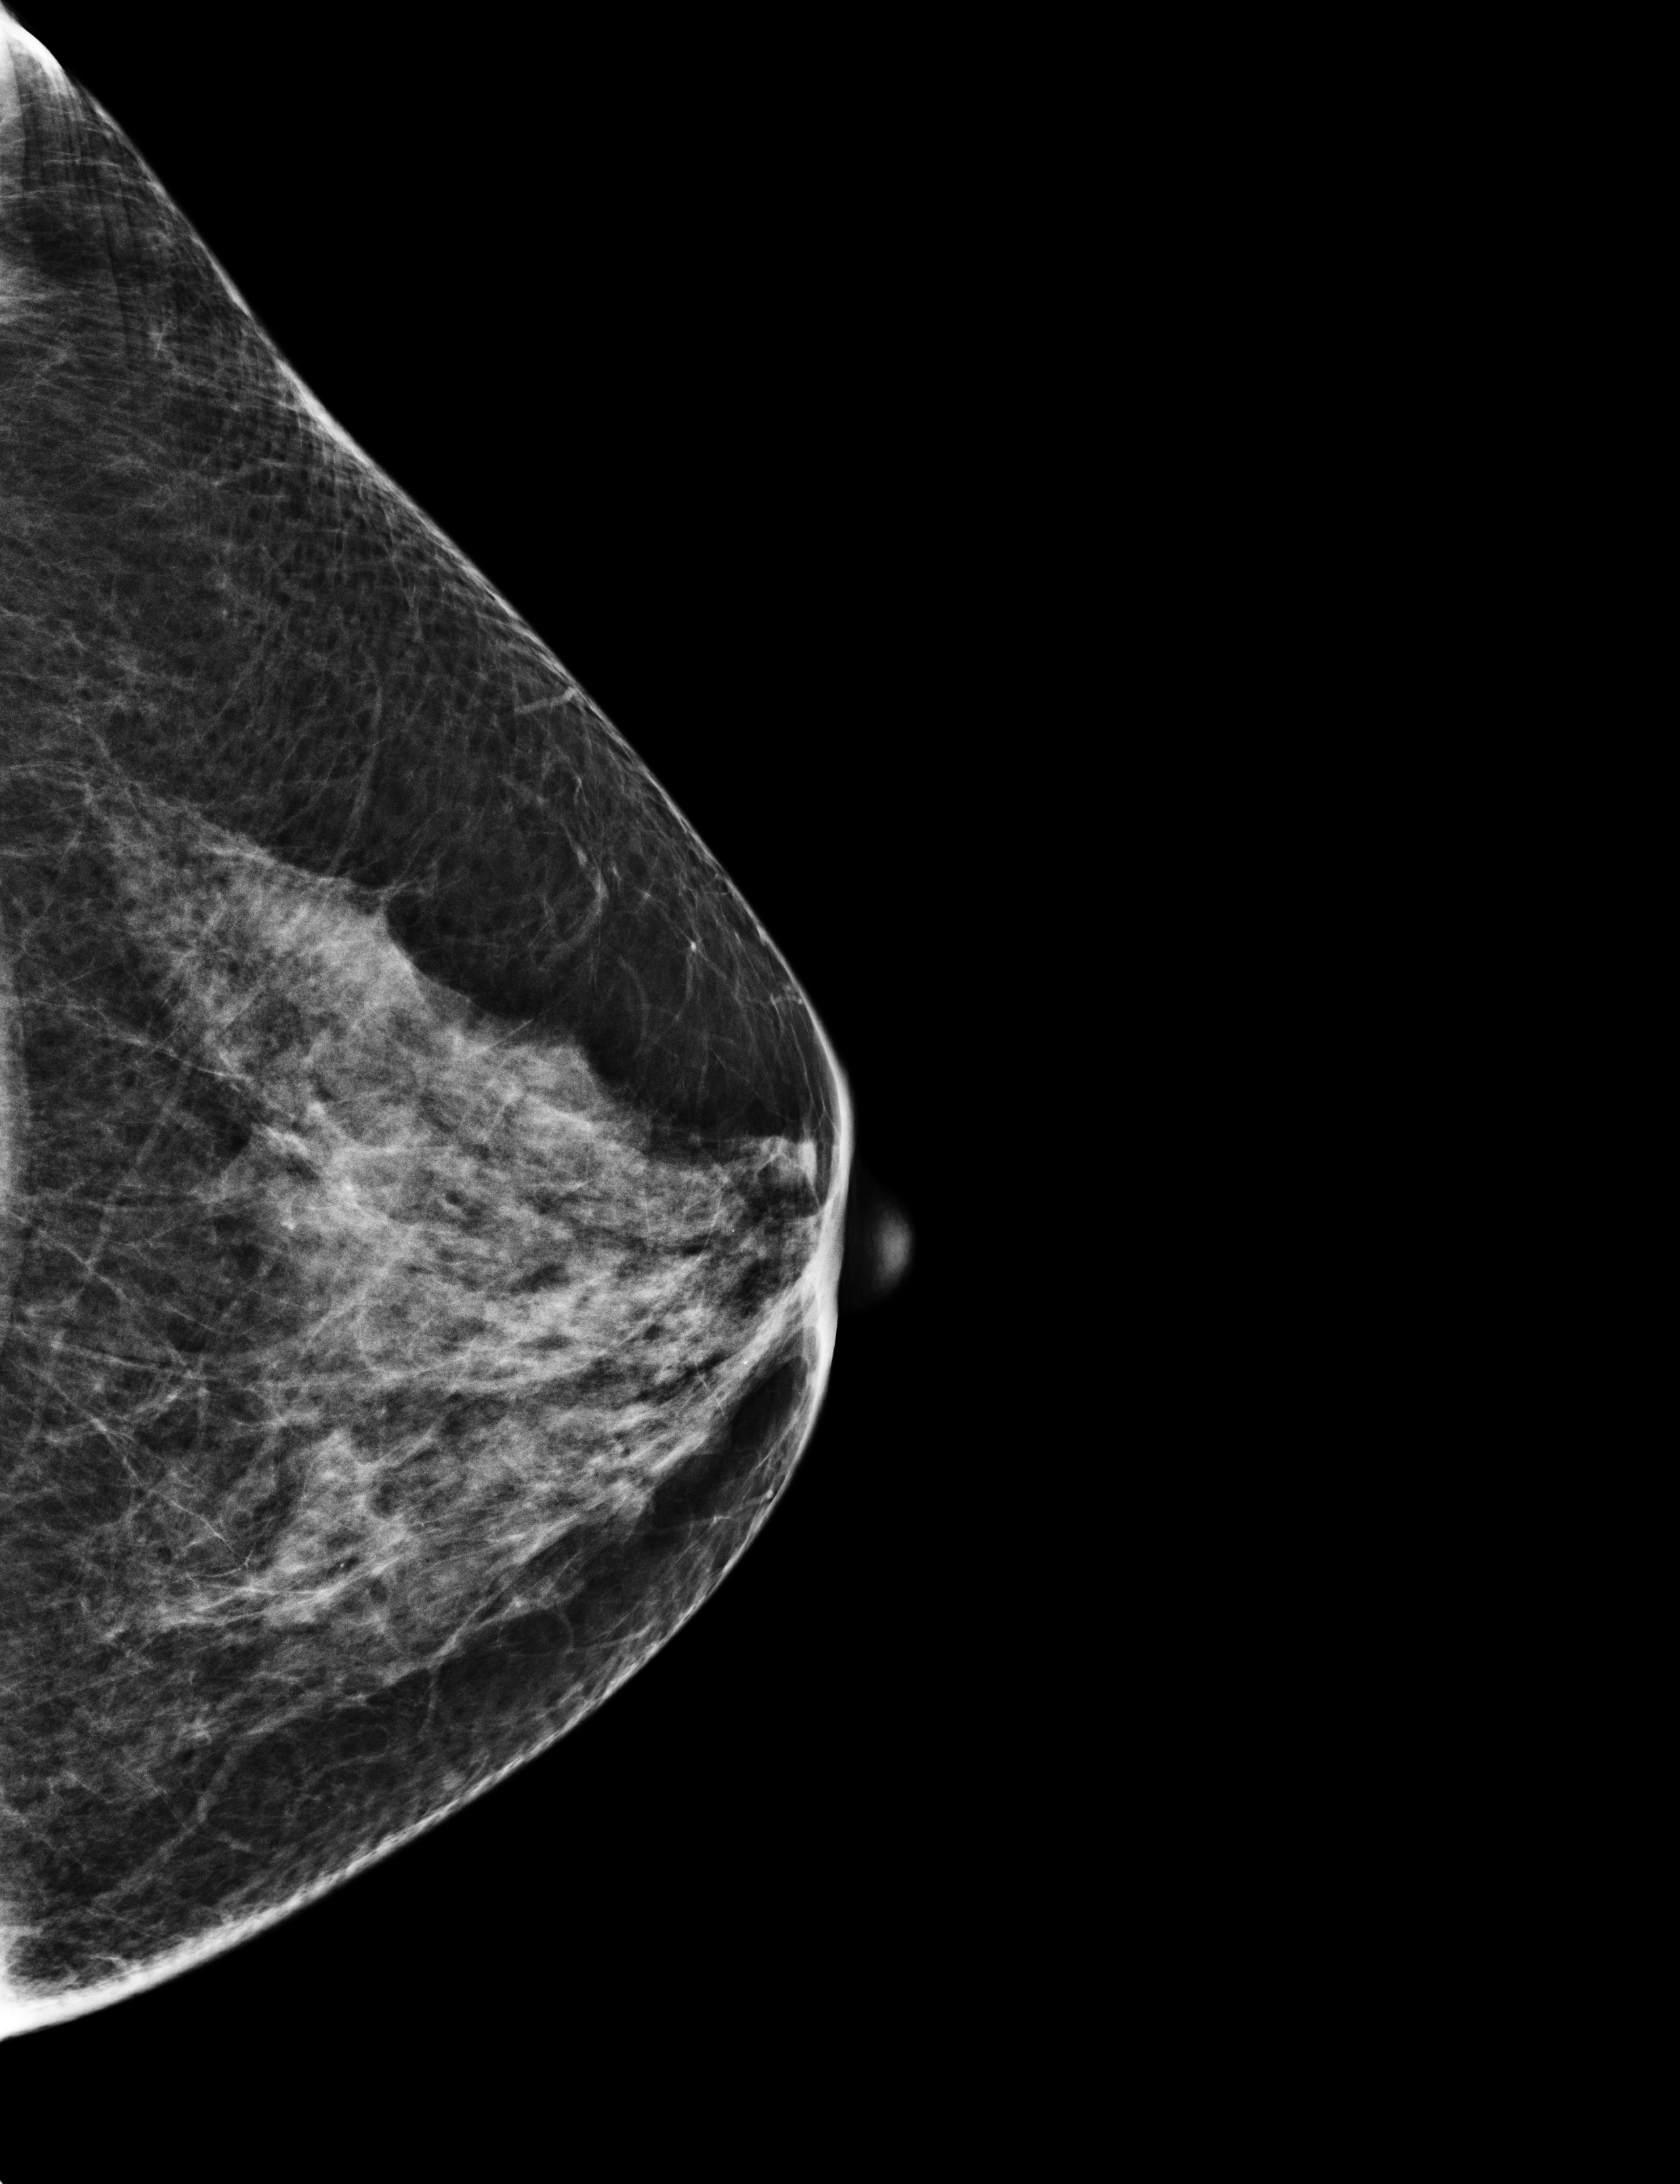
Annual screening mammography examination; compressed breast thickness 53 mm; system: Selenia Dimensions. Female patient, age 58 years.
Image type: full-field digital mammogram. Breast: left. Projection: cranio-caudal projection.